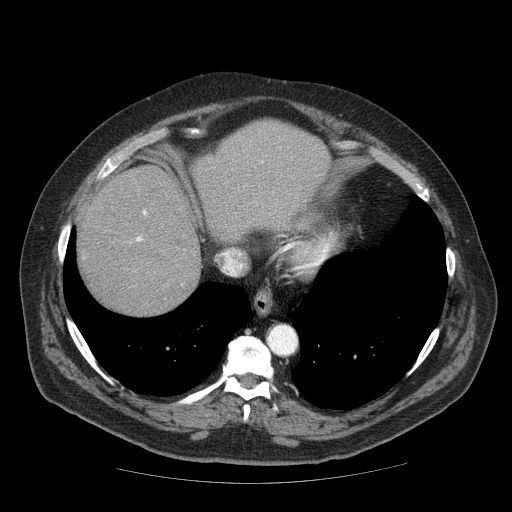
Contrast-enhanced abdominal CT (liver protocol), one axial slice. Position 60 of 85 along the scan axis. Soft-tissue window (W 400 / L 40 HU). 512 × 512 image matrix, field of view 420 × 420 mm. From the clinical record (not read from this slice): diagnosis: hepatocellular carcinoma (patient treated with transarterial chemoembolisation; whether this scan precedes or follows treatment is not stated here); TNM stage (as recorded): Stage-IIIA; Child-Pugh class: A; tumour nodularity: multinodular.
Annotated regions visible in this slice (semi-automatically segmented with operator editing):
- abdominal aorta: bounding box <268,326,296,355> (left, top, right, bottom; pixels)
- liver parenchyma outside the tumour (the mass and vessels are separate outlines, so this box may not span the whole liver): <78,120,330,314>
- liver vessels: <136,211,146,241>